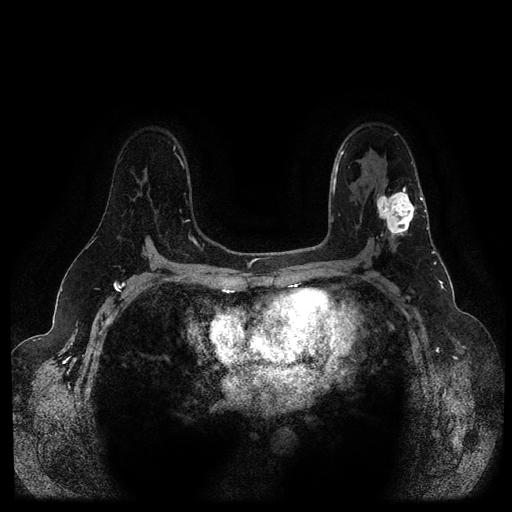
Breast MRI (dynamic contrast-enhanced, multi-phase), one axial slice; position 68 of 116 along the scan axis; dynamic contrast-enhanced series, time point 2 of 5 at this slice position (early post-contrast); 1.5 T; TE 2.6 ms, TR 5.3 ms; 512 × 512 image matrix, field of view 350 × 350 mm. Female patient, age 54 years.
Annotated regions visible in this slice (semi-automatic segmentation, software-assisted and operator-edited):
- breast lesion (labelled 'tumour' in the annotation; benign lesions carry a separate 'benign' label): bounding box [x1, y1, x2, y2] px = [376, 185, 418, 243]